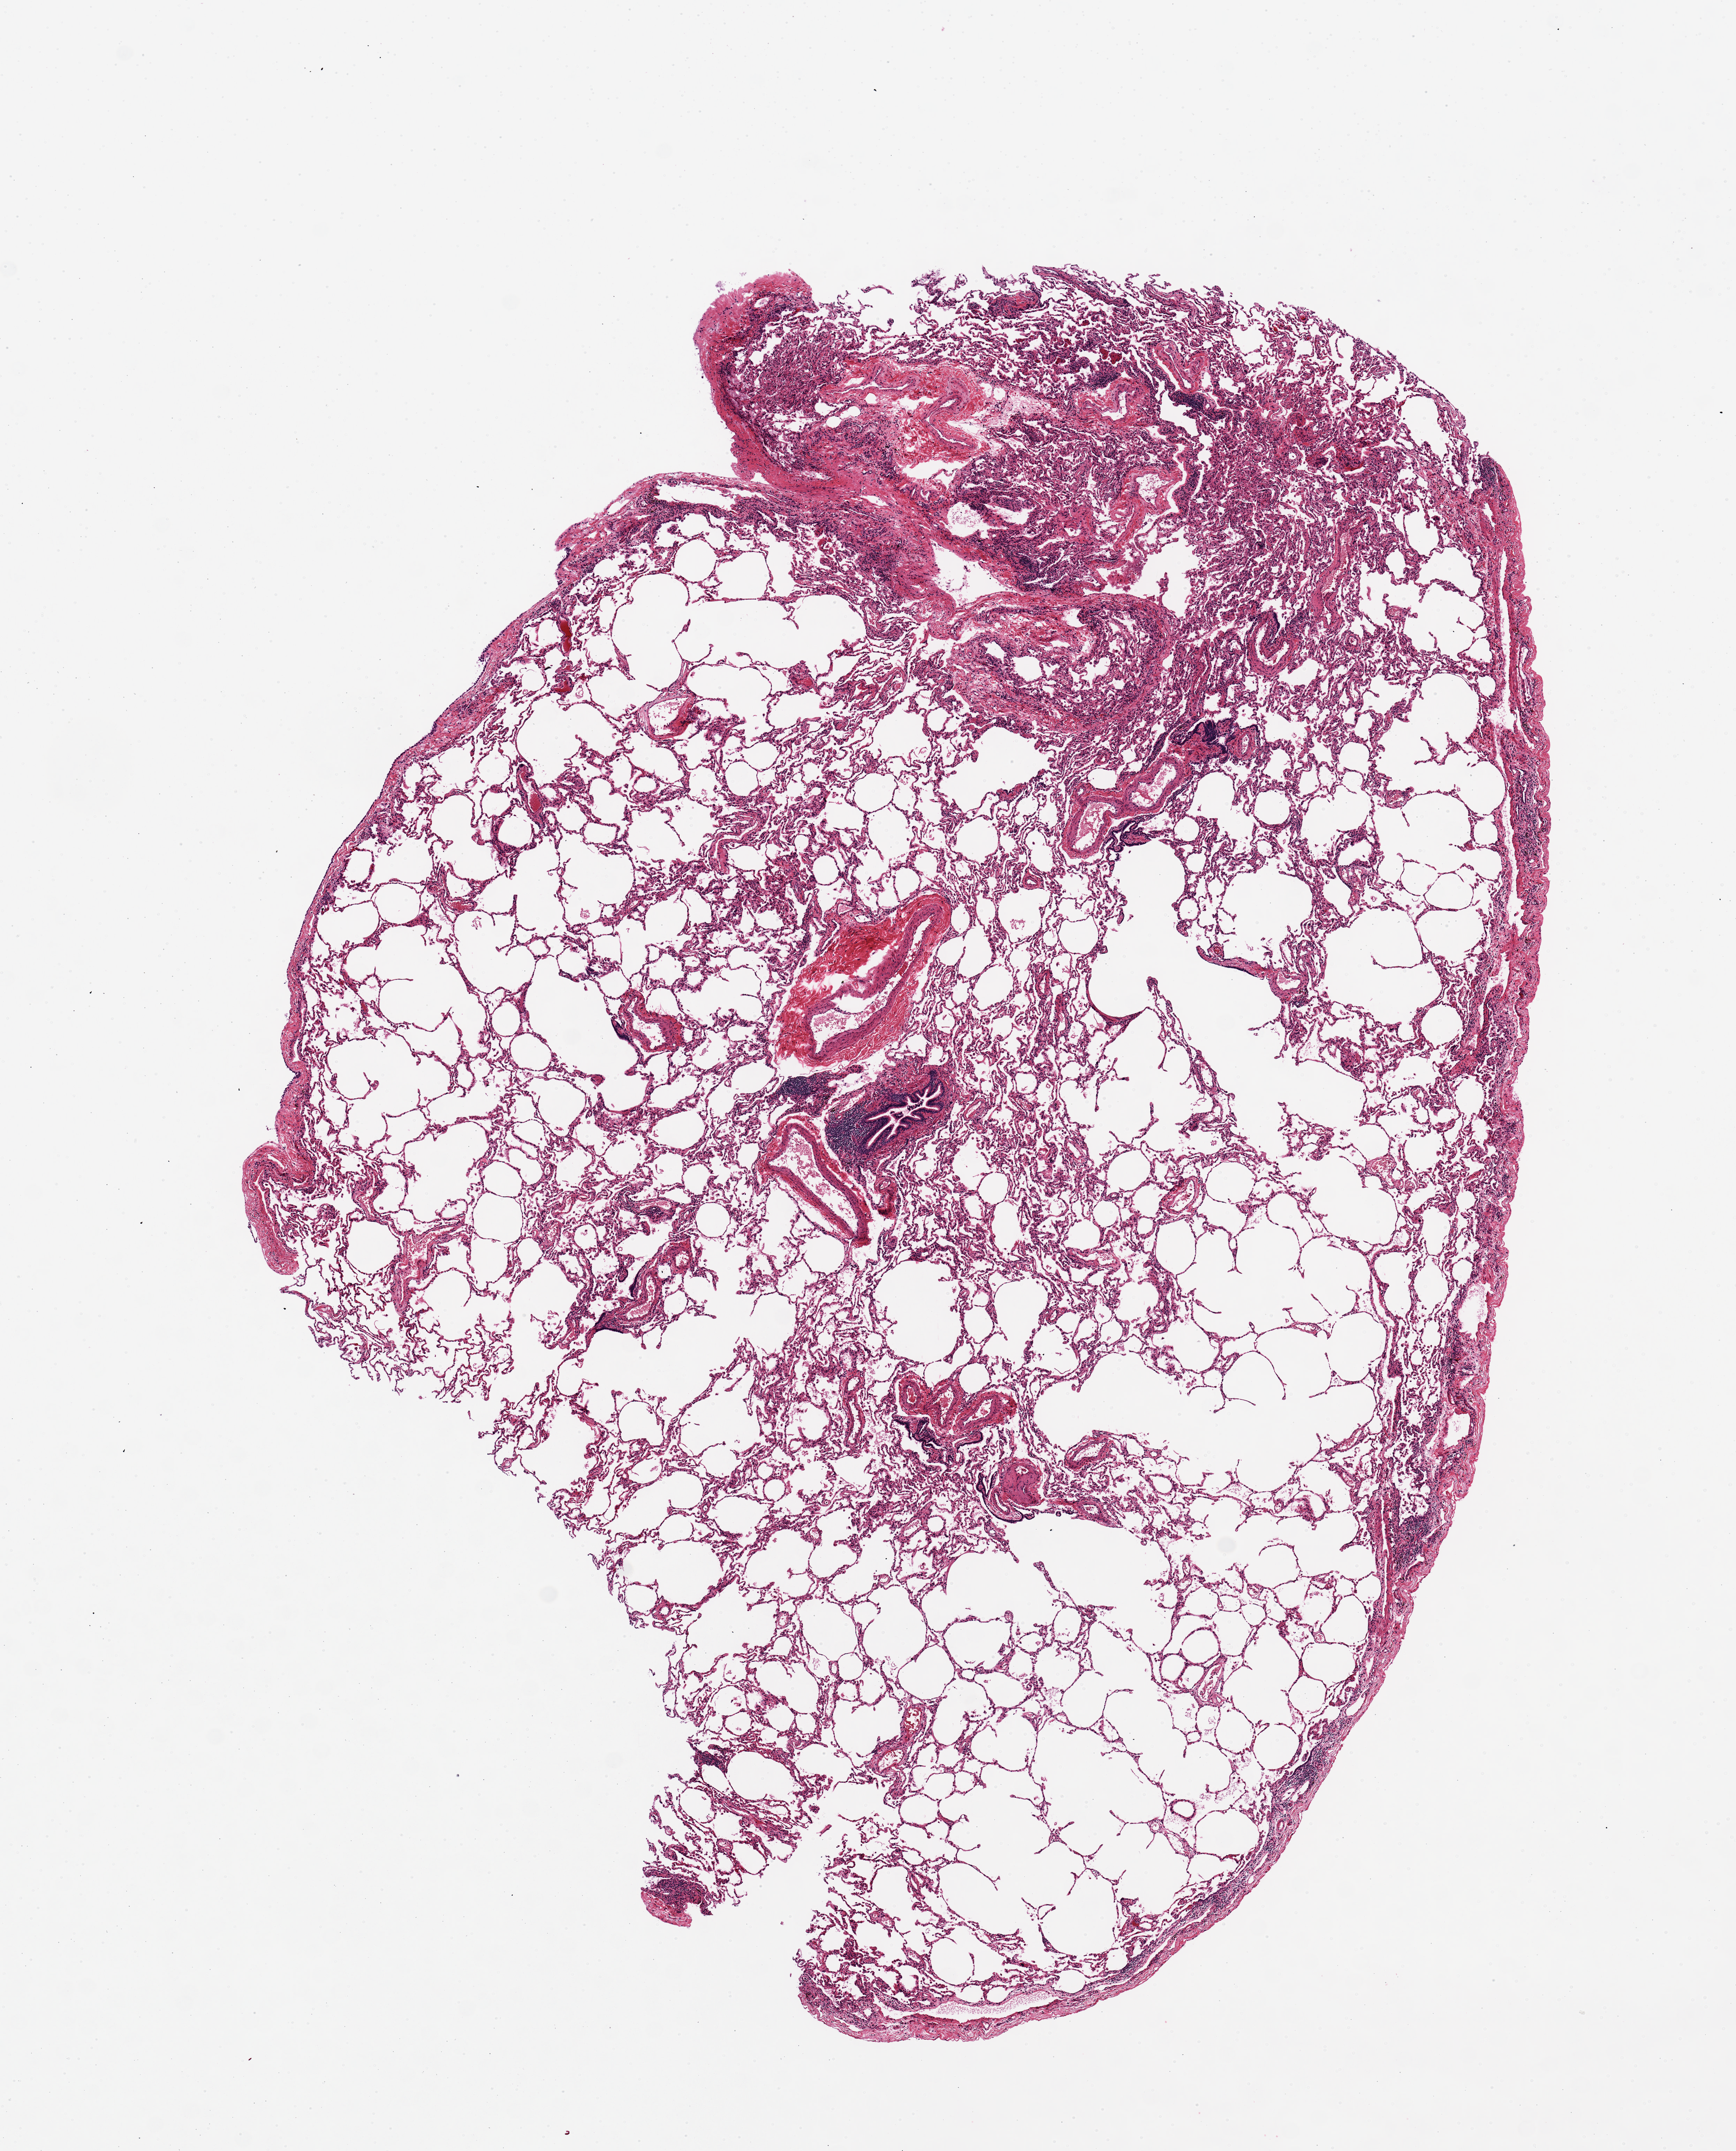
Digitized haematoxylin and eosin-stained section, brightfield, shown as a low-resolution overview of the whole scanned area (about 9.8 x 12.2 mm, from a 20x scan). PAXgene-fixed, paraffin-embedded tissue. Section of lung (target tissue). Tissue donor sample. Donor sex: female.
- review note (as recorded): Mild-moderate emphysema; focal atelectasis. Pleura sampled